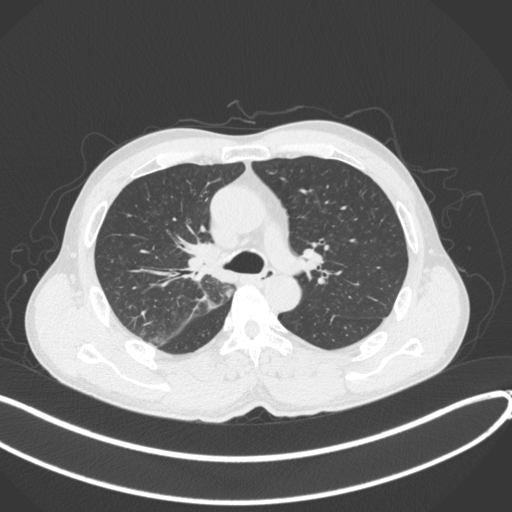
Chest CT, one axial slice. Position 256 of 409 along the scan axis. Reconstruction kernel B31f. 120 kVp. Lung window (W 1500 / L -600 HU). 512 × 512 image matrix, field of view 400 × 400 mm. Patient: male, 53 years. Case-level facts recorded for this patient, not image findings: clinical TNM (as recorded): T1b N0 M0.
Annotated regions visible in this slice (bounding box drawn by a radiologist):
- lung tumour (recorded histology: squamous cell carcinoma): bounding box (x1, y1, x2, y2) in pixels: (175, 239, 232, 285)